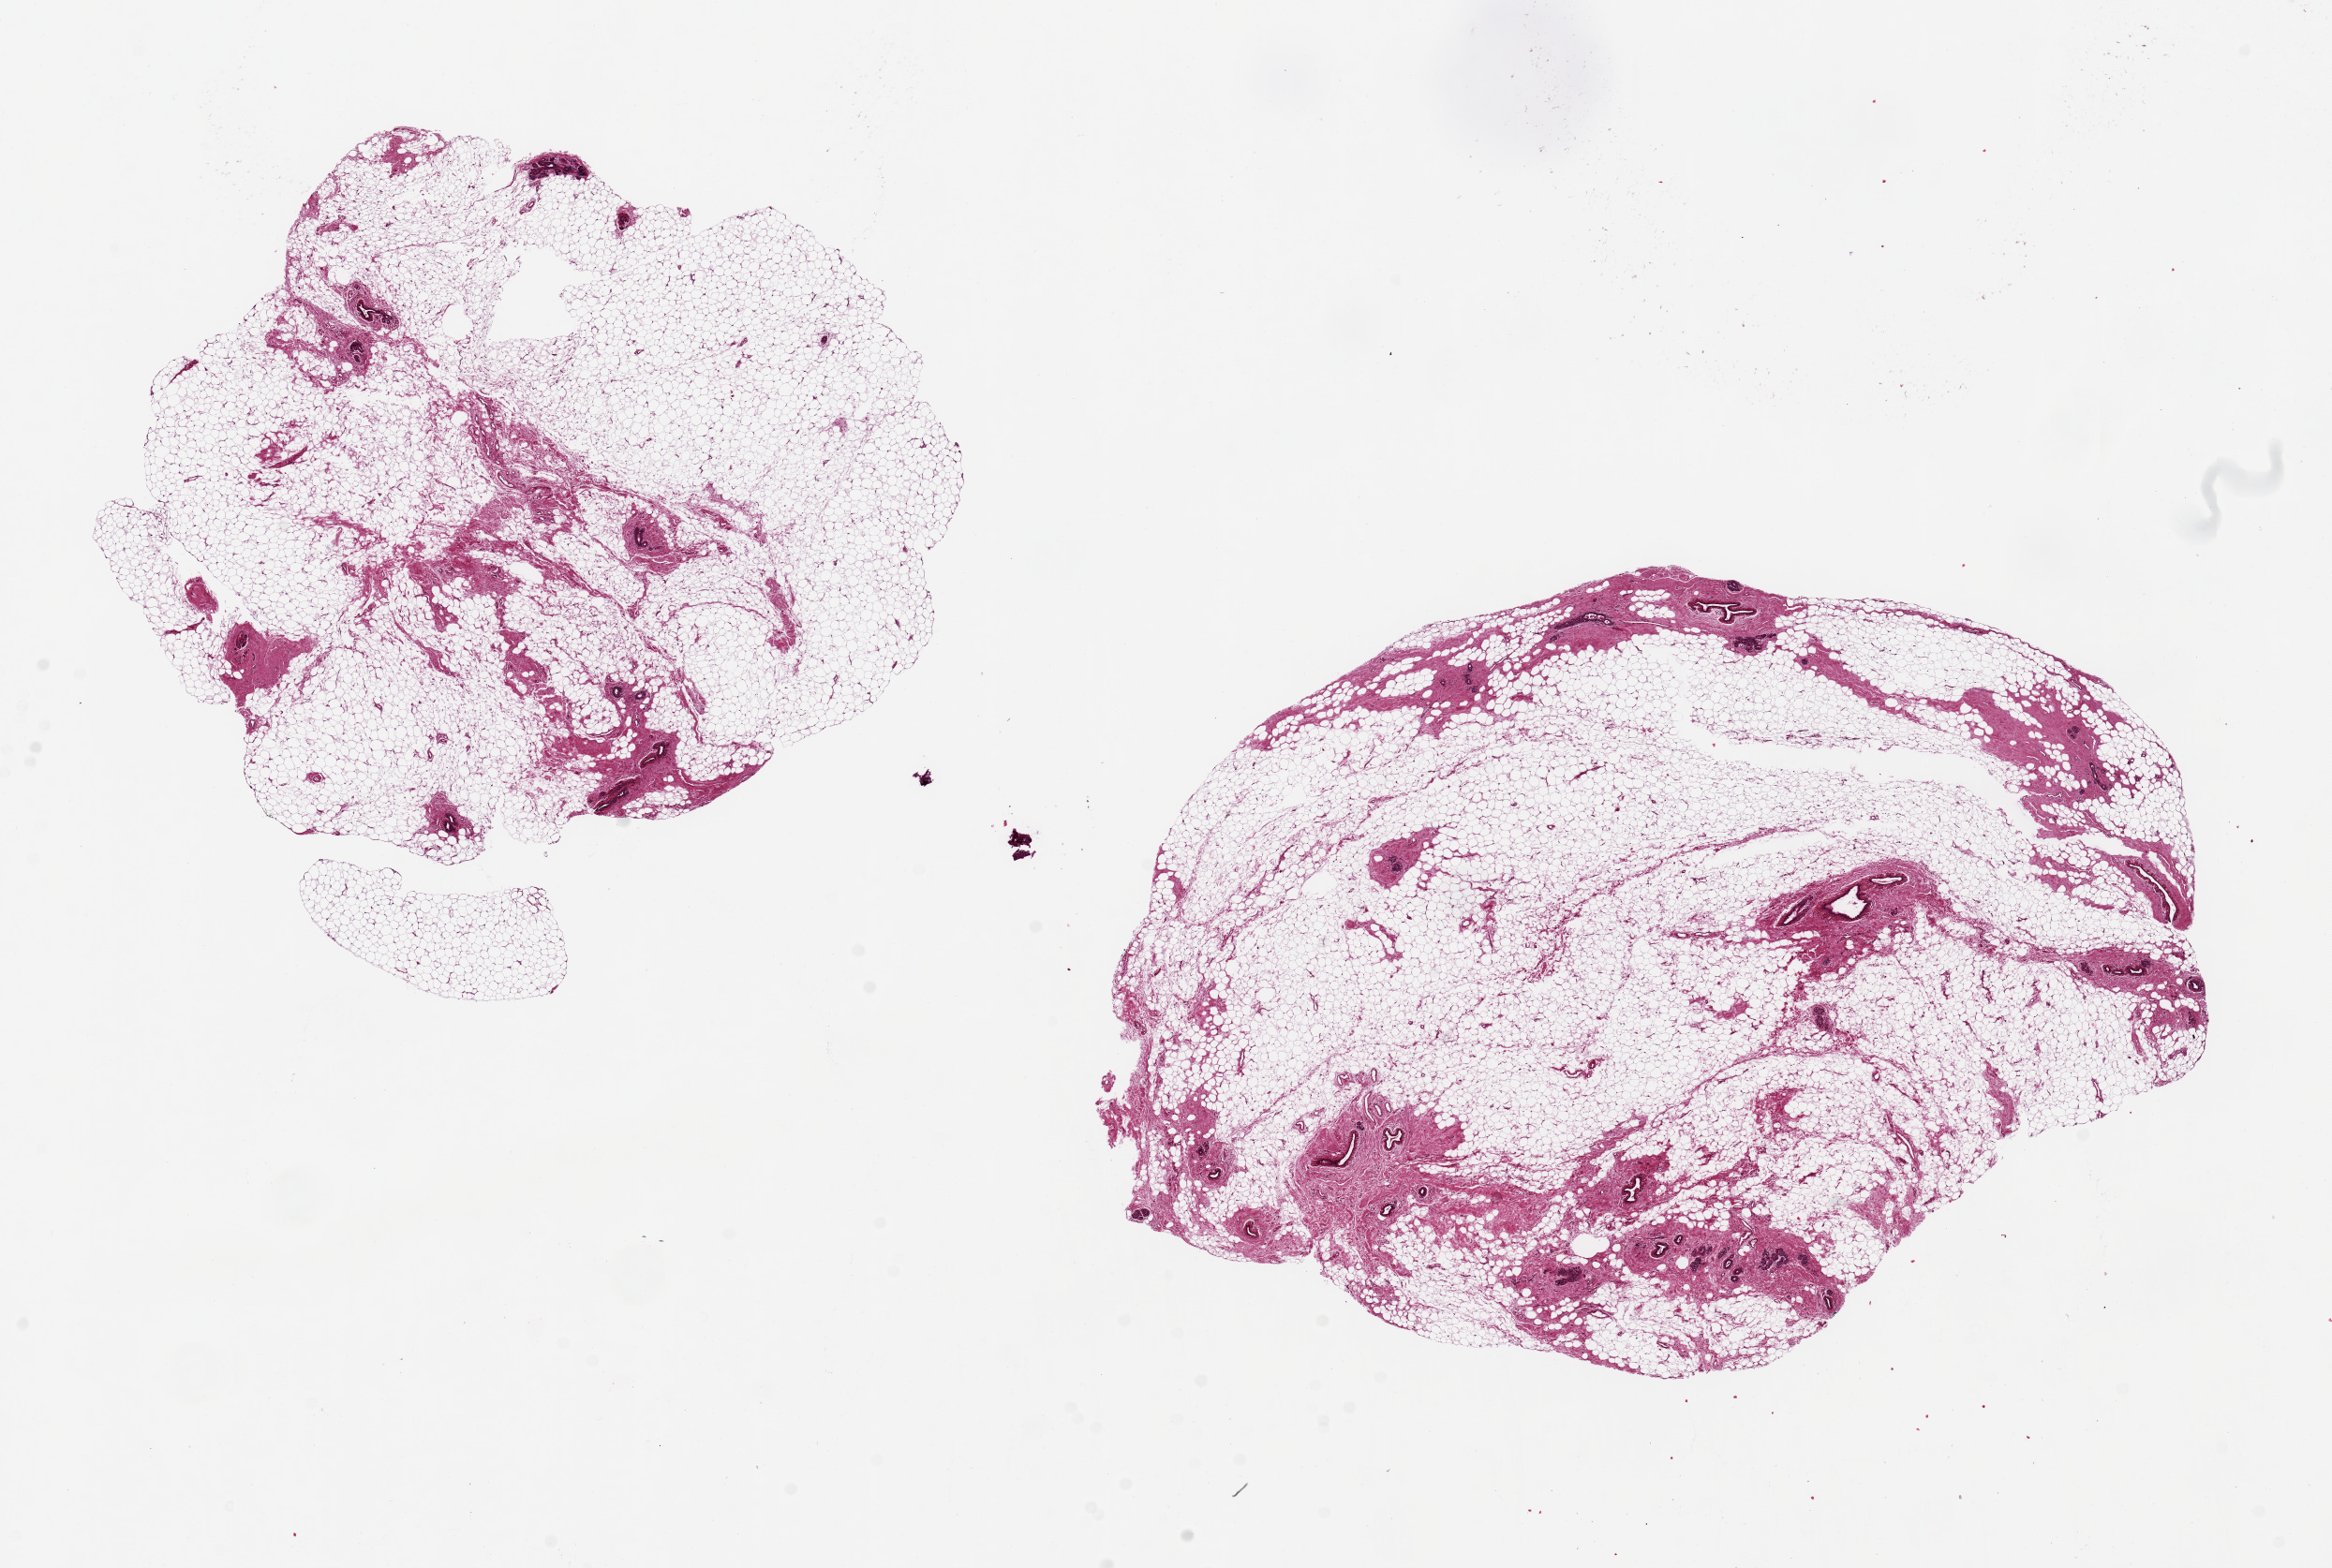
Whole-slide image, H&E stain, whole scanned area (about 19.7 x 13.2 mm, acquisition: 20x scan) shown as a low-resolution overview, PAXgene-fixed paraffin-embedded (PFPE) section, sampled site (target tissue): breast, tissue donor sample.
* reviewer comment on this tissue sample: 2 pieces, 9x7 & 7x7mm; atorphic TDLUs present